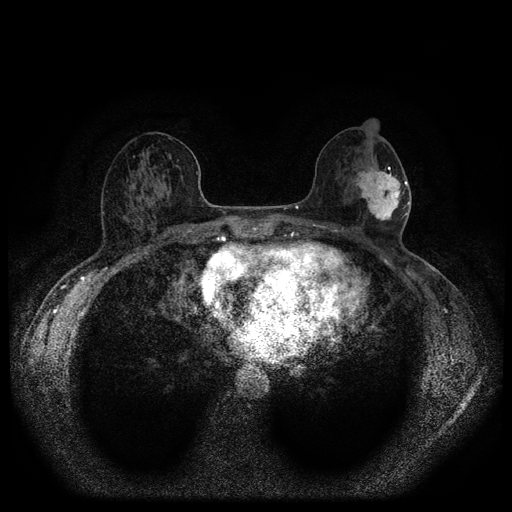
Breast MRI (dynamic contrast-enhanced, multi-phase), one axial slice; slice 50 of 116 in the series (ordered by position); dynamic contrast-enhanced series, time point 2 of 5 at this slice position (early post-contrast); 1.5 T; TE 2.7 ms, TR 5.4 ms; 2 mm slice thickness; 512 × 512 image matrix, field of view 330 × 330 mm. Patient: female, 56 years.
Outlined on this slice (semi-automatic segmentation, software-assisted and operator-edited):
- breast lesion (labelled 'tumour' in the annotation; benign lesions carry a separate 'benign' label): bounding box [x1, y1, x2, y2] px = [352, 165, 404, 224]